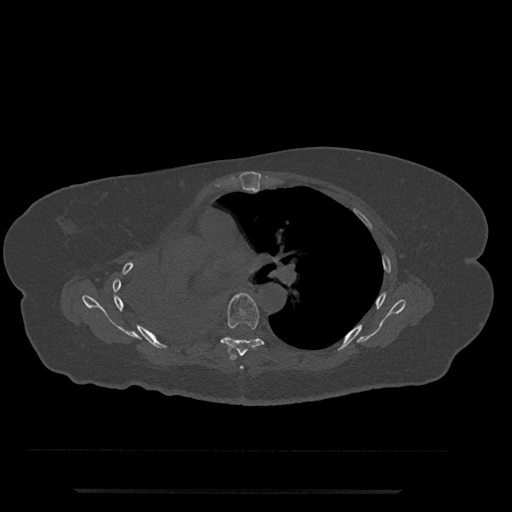
CT including the spine, one axial slice. Slice 493 of 797 in the series (ordered by position). Reconstruction kernel Br40s/3. Bone window (W 1800 / L 400 HU). 0.5 mm slice thickness. 512 × 512 image matrix. Patient: female, 51 years. Case-level facts recorded for this patient, not image findings: primary cancer: neuro; vertebrae with lytic lesions (as recorded): T8.
Outlined on this slice (semi-automatic segmentation, software-assisted and operator-edited):
- T5 vertebra: bounding box (x1, y1, x2, y2) in pixels: (240, 366, 243, 369)
- T6 vertebra: (221, 293, 264, 360)
- T7 vertebra: (227, 337, 231, 339)